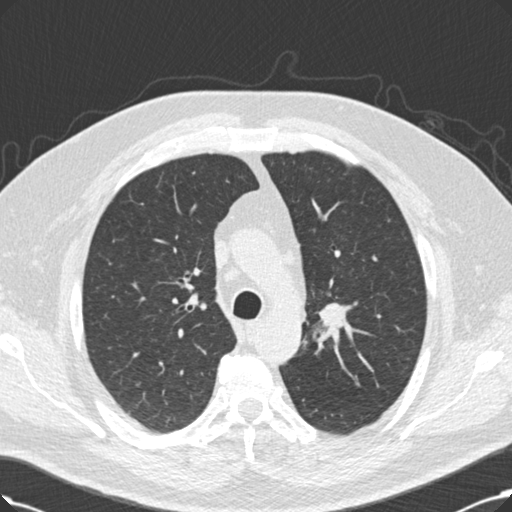
Low-dose screening chest CT, one axial slice. Position 158 of 214 along the scan axis. Lung window (W 1500 / L -600 HU). 512 × 512 image matrix, field of view 365 × 365 mm.
Structures marked on this image (manually delineated by an expert):
- lesion 1 (tumor): bounding box (x1, y1, x2, y2) in pixels: (319, 303, 357, 327)